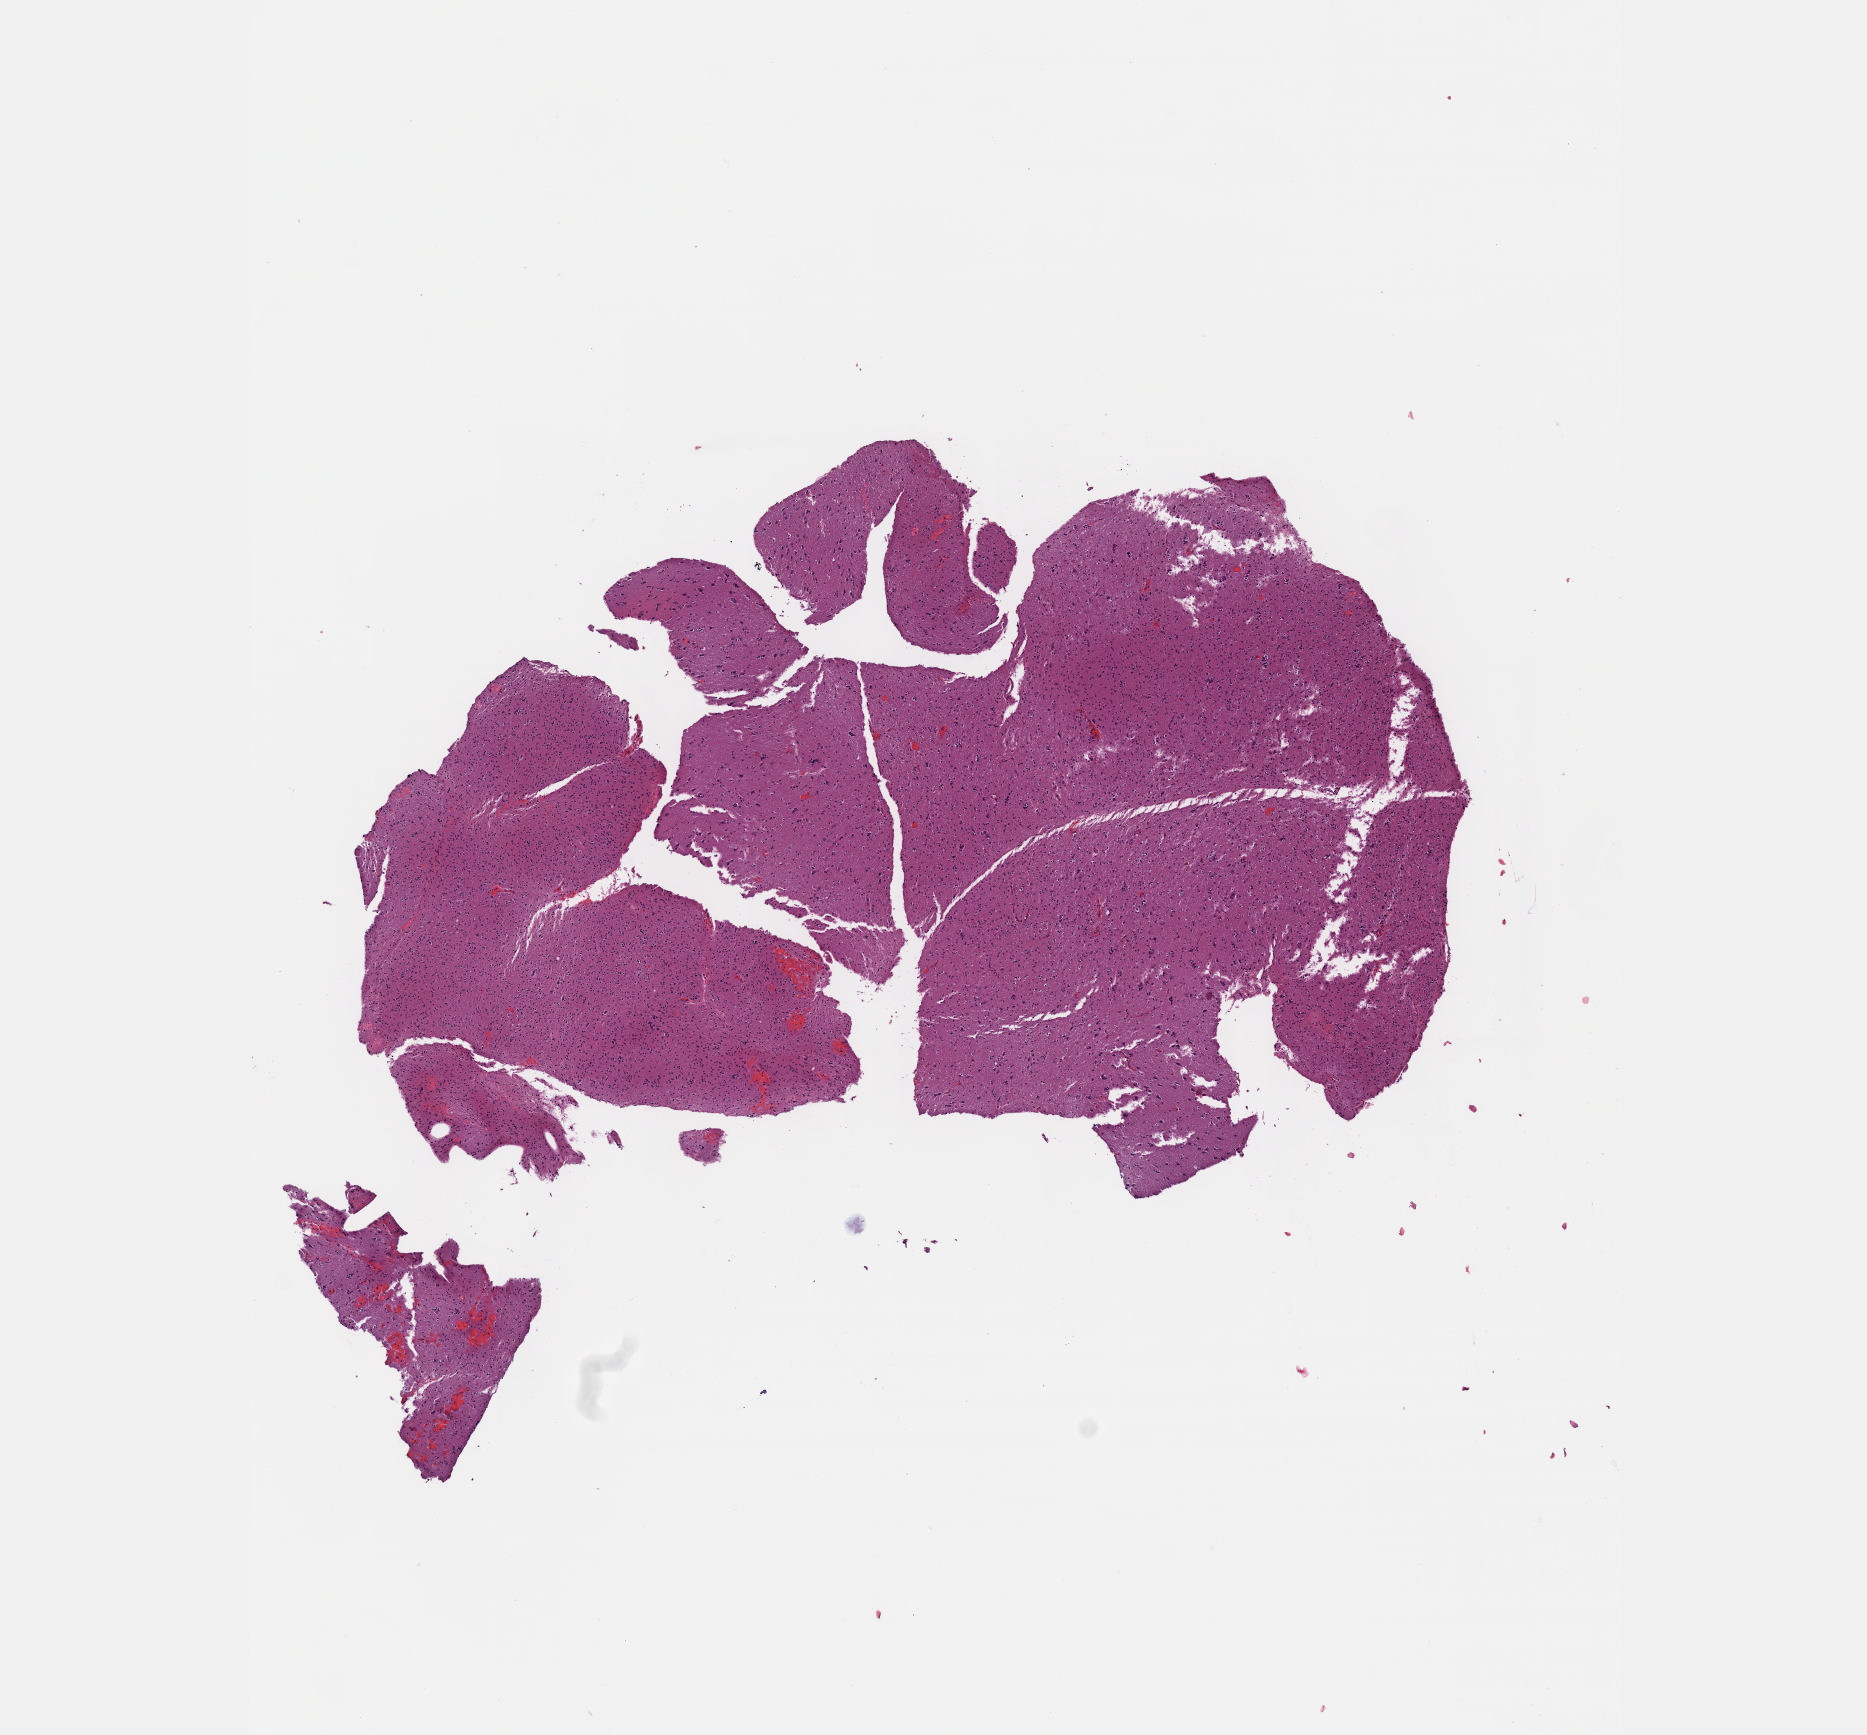
Whole-slide histology image, H&E-stained — shown as a low-resolution overview of the whole scanned area (about 7.5 x 7.0 mm), formalin-fixed paraffin-embedded (FFPE) diagnostic section, primary tumour sample from the brain. Male patient; age at initial diagnosis 38 years. Histologic grade: G2 (moderately differentiated).
Histologic diagnosis: Oligodendroglioma, NOS (cerebrum).